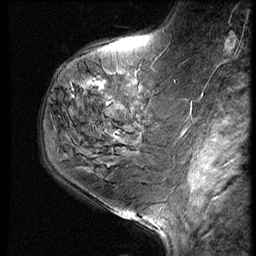
Breast MRI (dynamic contrast-enhanced), one sagittal slice; slice 23 of 60 in the series (ordered by position); 3 images stored at this slice position (order not interpretable as contrast timing); 1.5 T; TE 4.2 ms, TR 9 ms; 2.5 mm slice thickness; 256 × 256 image matrix, field of view 180 × 180 mm. Female patient, age 59 years. Case-level facts recorded for this patient, not image findings: setting: breast cancer imaged before/during neoadjuvant chemotherapy; receptor status: HER2-positive.
Annotated regions visible in this slice (semi-automatic segmentation, software-assisted and operator-edited):
- analysis volume of interest (the breast-tissue region the enhancement analysis was run in; not a lesion): bounding box (x1, y1, x2, y2) in pixels: (78, 61, 161, 125)
- tumour enhancement mask (voxels above the 140 % enhancement threshold inside the analysis volume of interest): (91, 82, 103, 88)